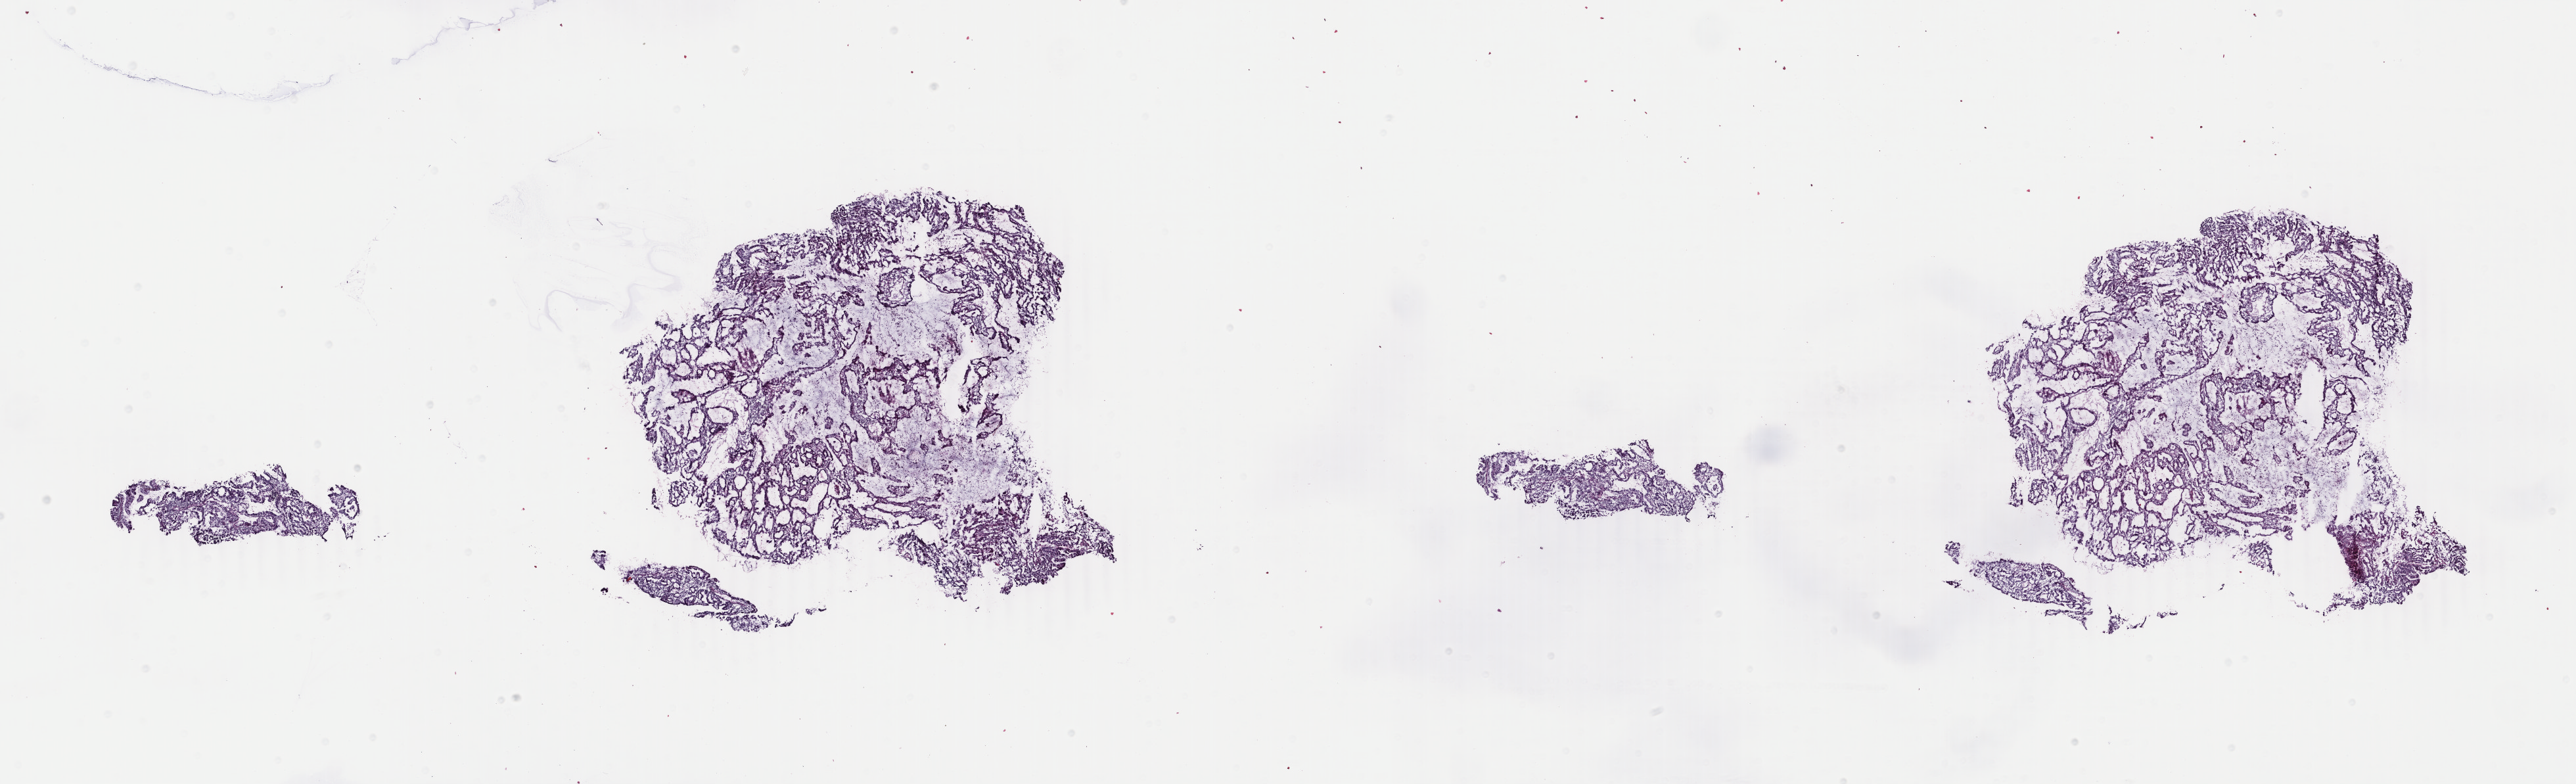
H&E whole-slide image, whole scanned area (about 31.2 x 9.5 mm, slide scanned at 40x) shown as a low-resolution overview; frozen section from the bottom of the tissue portion; primary tumour sample from the uterus. Patient: female, age at initial diagnosis 54 years. Histologic grade: G1 (well differentiated). Slide review estimates, as recorded: tumour cells 100%, tumour nuclei 75%, normal cells 0%, stromal cells 0%, necrosis 0%. Inflammatory infiltration, as recorded: lymphocyte infiltration 0%, monocyte infiltration 0%, neutrophil infiltration 0%.
• FIGO stage: IIIA
• diagnosis: Endometrioid adenocarcinoma, NOS (endometrium)